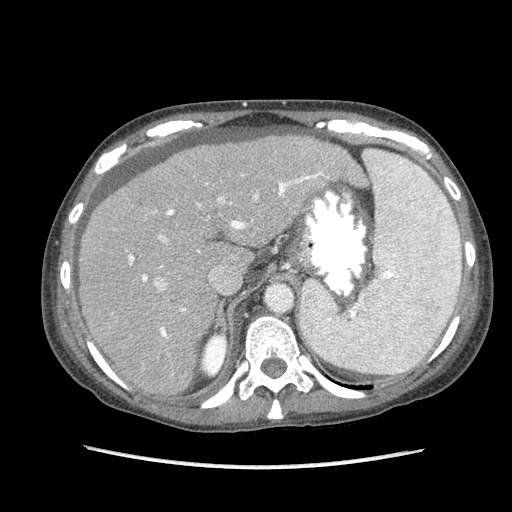
Contrast-enhanced abdominal CT (liver protocol), one axial slice; position 63 of 87 along the scan axis; 120 kVp; soft-tissue window (W 400 / L 40 HU); 2.5 mm slice thickness; 512 × 512 image matrix, field of view 340 × 340 mm. Case-level facts recorded for this patient, not image findings: diagnosis: hepatocellular carcinoma (patient treated with transarterial chemoembolisation; whether this scan precedes or follows treatment is not stated here); TNM stage (as recorded): Stage-IIIB; Child-Pugh class: A; tumour differentiation: no biopsy.
Annotated regions visible in this slice (semi-automatically segmented with operator editing):
- abdominal aorta: bounding box (x1, y1, x2, y2) in pixels: (267, 285, 292, 311)
- liver parenchyma outside the tumour (the mass and vessels are separate outlines, so this box may not span the whole liver): (78, 134, 366, 394)
- mass: (113, 193, 130, 214)
- liver vessels: (128, 171, 330, 338)